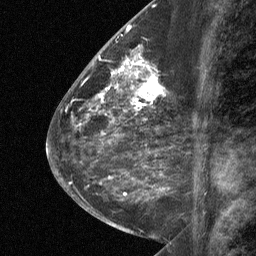
Breast MRI (dynamic contrast-enhanced), one sagittal slice; slice 27 of 64 in the series (ordered by position); dynamic contrast-enhanced study with each time point stored as its own series, time point 2 of 3 at this slice position (early post-contrast, ordered by acquisition time); 1.5 T; TE 4.8 ms, TR 27 ms; 256 × 256 image matrix, field of view 180 × 180 mm. Patient: female, 59 years. From the clinical record (not read from this slice): setting: breast cancer imaged before/during neoadjuvant chemotherapy; receptor status: triple-negative.
Outlined on this slice (semi-automatically segmented with operator editing):
- analysis volume of interest (the breast-tissue region the enhancement analysis was run in; not a lesion): bounding box [x1, y1, x2, y2] px = [122, 58, 176, 109]
- tumour enhancement mask (voxels above the 90 % enhancement threshold inside the analysis volume of interest): [122, 58, 163, 105]